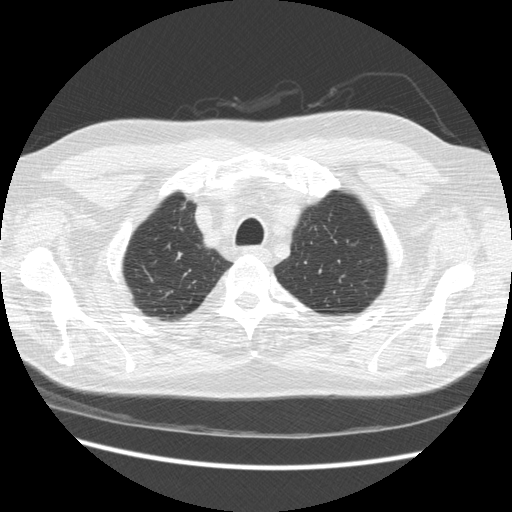
Axial slice from a low-dose chest CT screening exam, third annual screen, lung window (W 1500 / L -600 HU), 2.5 mm slice thickness, 120 kVp, slice 39 of 234 in the series, 512 × 512 image matrix. Male, age 66 years at enrolment. Former smoker at enrolment.
• Lesion marked by an expert reader, bounding box [x1, y1, x2, y2] px = [167, 190, 205, 223].
• Screening reader's record for this exam: no non-calcified nodule ≥4 mm recorded.
• Later outcome: lung cancer diagnosed 229 days after this screen — bronchiolo-alveolar adenocarcinoma, NOS, right upper lobe, moderately differentiated (G2), stage IA (AJCC 6th edition), 12 mm at pathology.